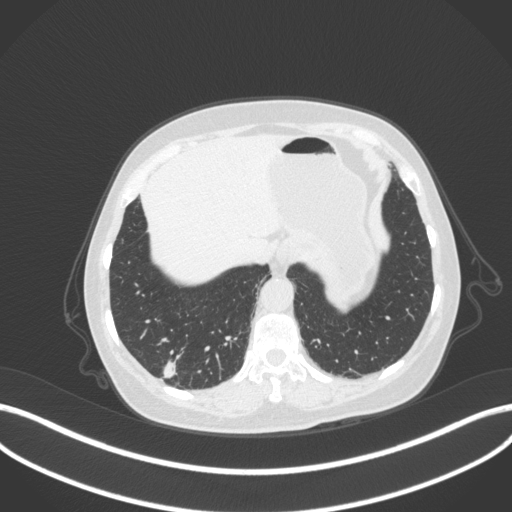
Chest CT, one axial slice. Slice 49 of 340 in the series (ordered by position). Reconstruction kernel B31f. Lung window (W 1500 / L -600 HU). 1 mm slice thickness. 512 × 512 image matrix. Female patient, age 69 years. Case-level facts recorded for this patient, not image findings: clinical TNM (as recorded): T1b N0 M0; histopathological grade: G2-3.
Outlined on this slice (rectangle marked by the reading radiologist):
- lung tumour (recorded histology: adenocarcinoma): bounding box [x1, y1, x2, y2] px = [158, 357, 179, 385]